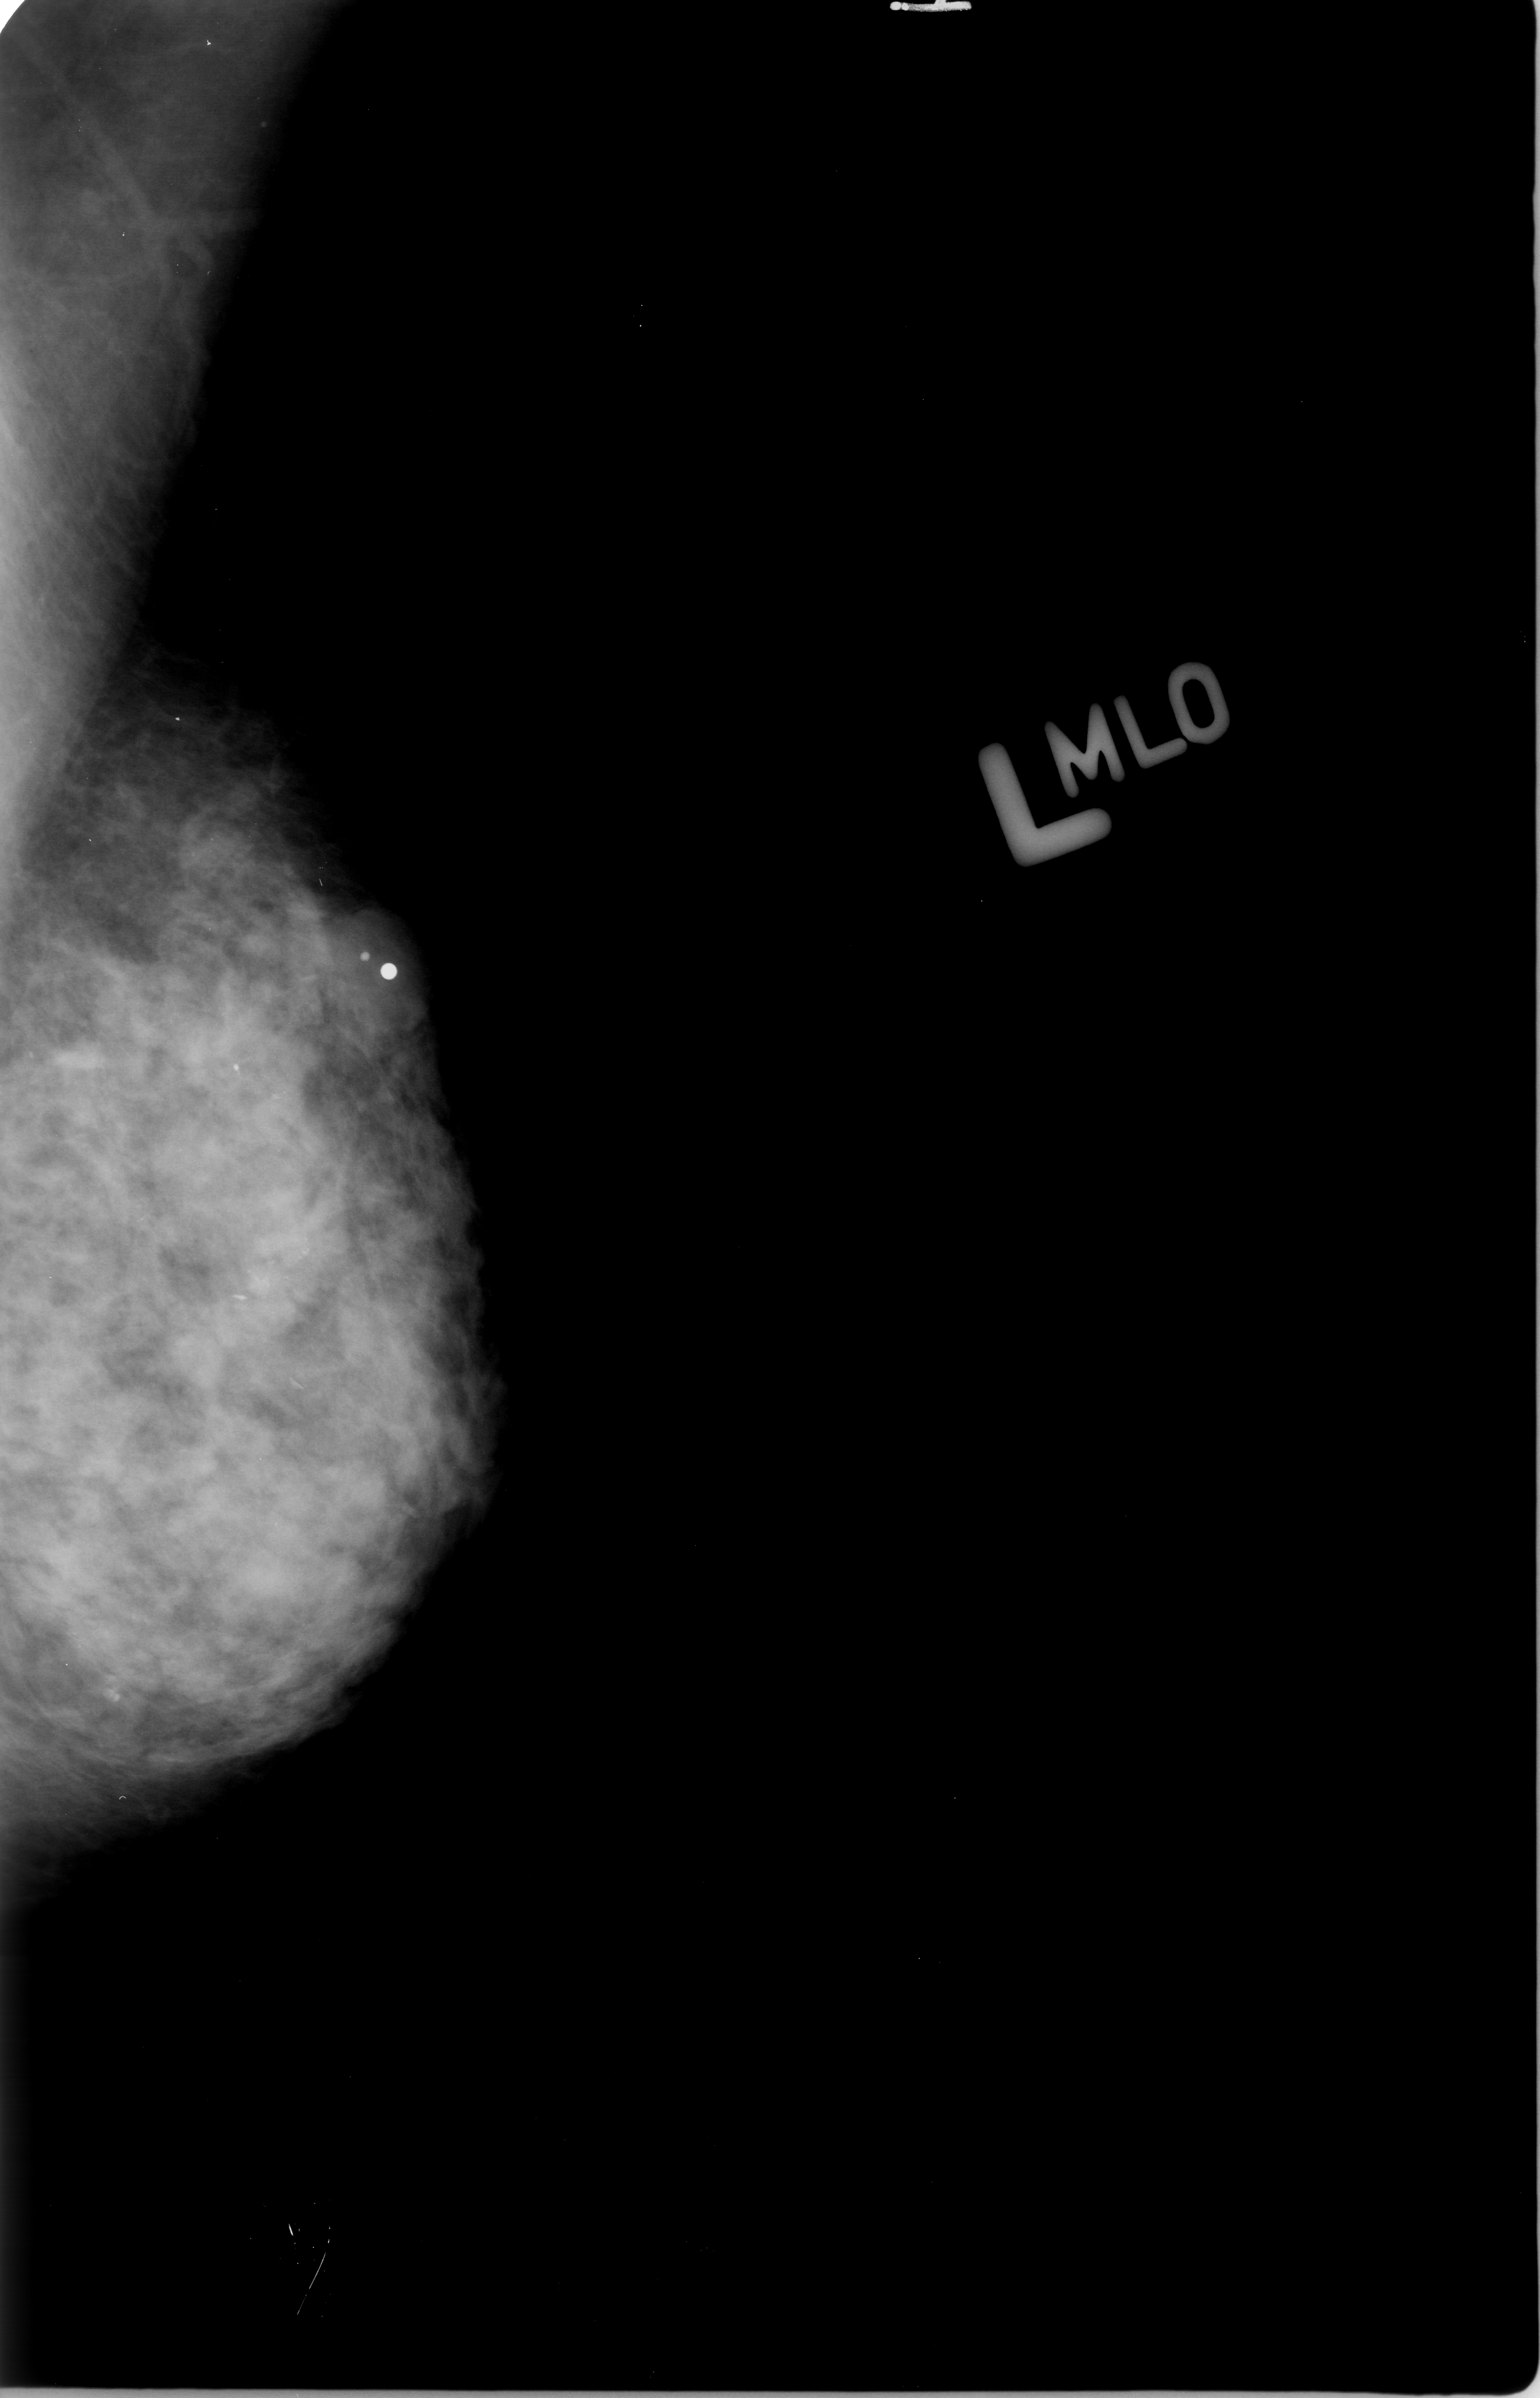
Digitized screen-film mammogram; left breast; mediolateral oblique (MLO) view; BI-RADS breast density category 3 (scale 1–4).
Radiologist-marked abnormalities on this image: calcifications, morphology pleomorphic, distribution clustered; BI-RADS assessment category 3; pathology (as recorded): malignant.